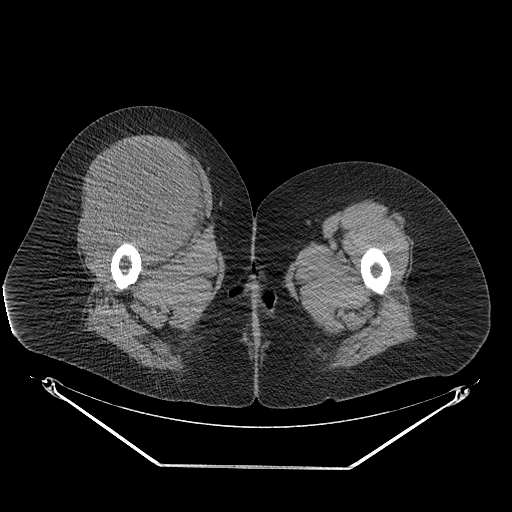
CT of an extremity soft-tissue mass (from a PET/CT study), one axial slice. Slice 45 of 267 in the series (ordered by position). Reconstruction kernel STANDARD. 140 kVp. Soft-tissue window (W 400 / L 40 HU). 512 × 512 image matrix, field of view 500 × 500 mm. Female patient. Case-level facts recorded for this patient, not image findings: histological type: malignant solitary fibrous tumor; grade: intermediate; site of the primary tumour: right thigh.
Outlined on this slice (expert contour drawn on MRI and transferred to this co-registered scan by the dataset authors):
- gross tumour volume including surrounding oedema: bounding box (x1, y1, x2, y2) in pixels: (77, 142, 207, 241)
- gross tumour volume (mass): (82, 142, 204, 239)